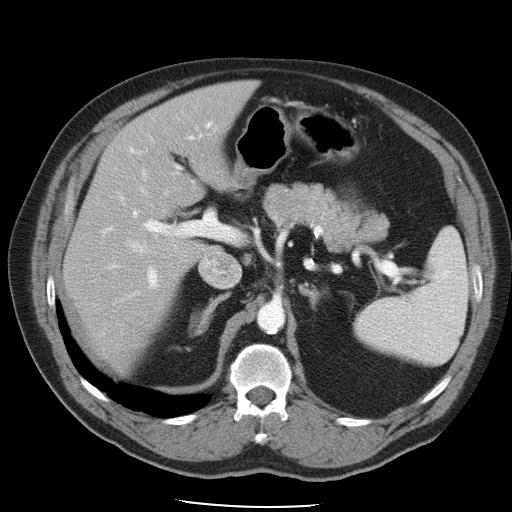
Contrast-enhanced abdominal CT, one axial slice; reconstruction kernel STANDARD; intravenous contrast given; soft-tissue window (W 400 / L 40 HU); 5 mm slice thickness; 512 × 512 image matrix, field of view 395 × 395 mm. Male patient, age 68 years. Case-level facts recorded for this patient, not image findings: diagnosis: colorectal cancer liver metastases, imaged before liver resection; multiple liver metastases: yes; largest metastasis: 1.7 cm; disease in both lobes: no.
Annotated regions visible in this slice (manually delineated by an expert):
- hepatic veins: bounding box [x1, y1, x2, y2] px = [122, 168, 239, 300]
- liver: [66, 81, 255, 368]
- planned liver remnant (the part of the liver to remain after resection): [67, 82, 255, 368]
- portal vein (with intrahepatic branches): [102, 123, 212, 289]